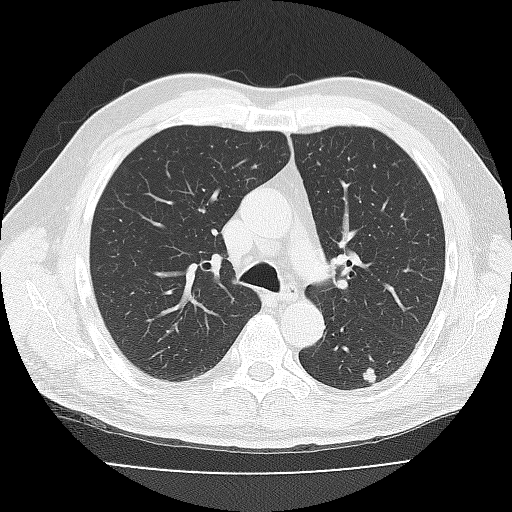
Low-dose screening chest CT, axial slice; second screening round (one year after baseline); lung window (W 1500 / L -600 HU); 120 kVp; slice 34 of 96 in the series; 512 × 512 image matrix, field of view 359 × 359 mm. Male, age 65 years at enrolment. Former smoker at enrolment.
- Lesion marked by an expert reader, bounding box (x1, y1, x2, y2) in pixels: (351, 356, 394, 396).
- The exam's reader record, not a measurement of the box and not confirmed to be the same lesion: non-calcified nodule or mass ≥4 mm, left lower lobe, 11 × 10 mm, smooth margins, soft tissue attenuation, pre-existing on the prior screen: yes; interval growth: yes.
- Official screen result: positive, other.
- Lung cancer was diagnosed 8 days after this screen: adenocarcinoma, NOS, left lower lobe, well differentiated (G1), stage IB (AJCC 6th edition), 10 mm at pathology.